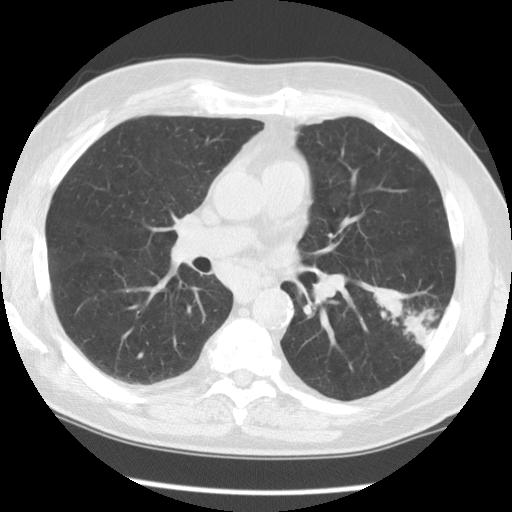
Chest CT (low-dose screening protocol), one axial image, baseline screening round, lung window (W 1500 / L -600 HU), 2.5 mm slice thickness, 512 × 512 image matrix, field of view 340 × 340 mm. Male participant, aged 71 years at enrolment. Former smoker at enrolment.
Expert reader's lesion annotation, bounding box (x1, y1, x2, y2) in pixels: (370, 278, 459, 365). The screening reader recorded 3 non-calcified nodules or masses ≥4 mm on this exam (left lower lobe, right upper lobe, right upper lobe); which of them this box marks is not recorded. Official screen result: positive, change unspecified: nodule(s) >= 4 mm or enlarging nodule(s), mass(es), or other non-specific abnormalities suspicious for lung cancer. Lung cancer was diagnosed 42 days after this screen: small cell carcinoma, NOS, left lower lobe, poorly differentiated (G3), stage IIIA (AJCC 6th edition), 19 mm at pathology.